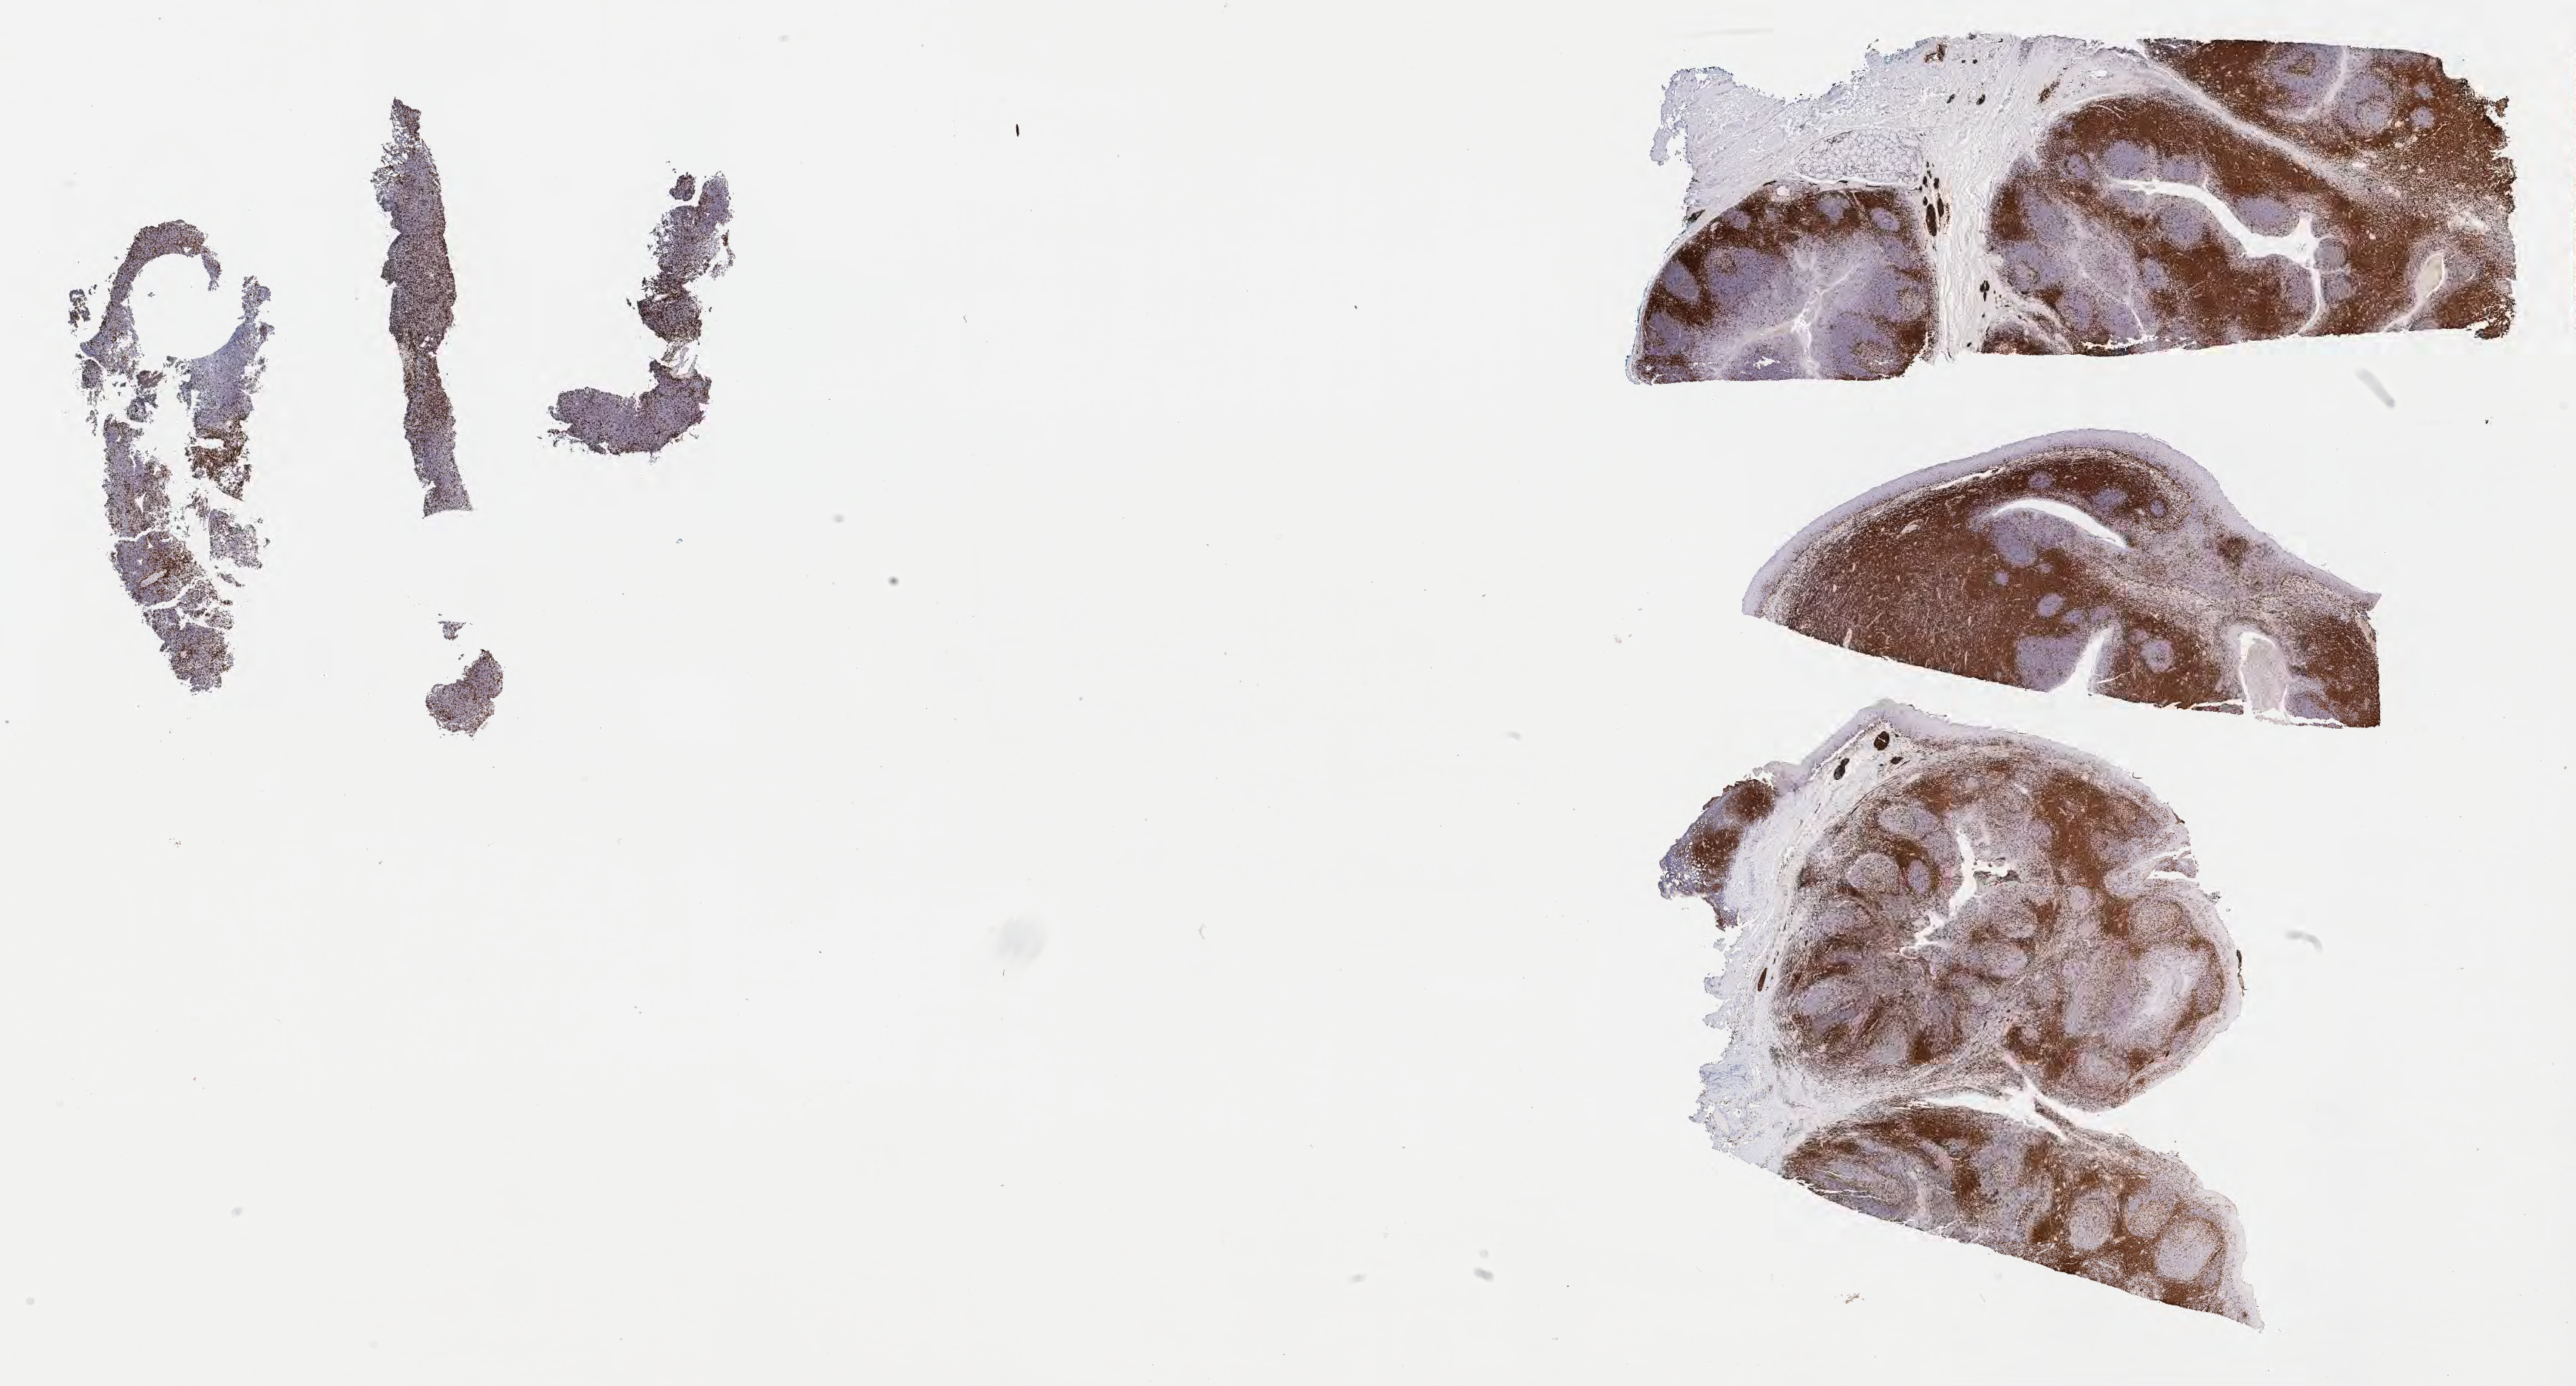
IHC for CD3, whole-slide image, whole scanned area (about 28.2 x 15.2 mm) shown as a low-resolution overview. Tumor tissue. Anatomic site: spleen. Patient: male, age at initial diagnosis 8 years.
• diagnosis: Burkitt lymphoma, NOS